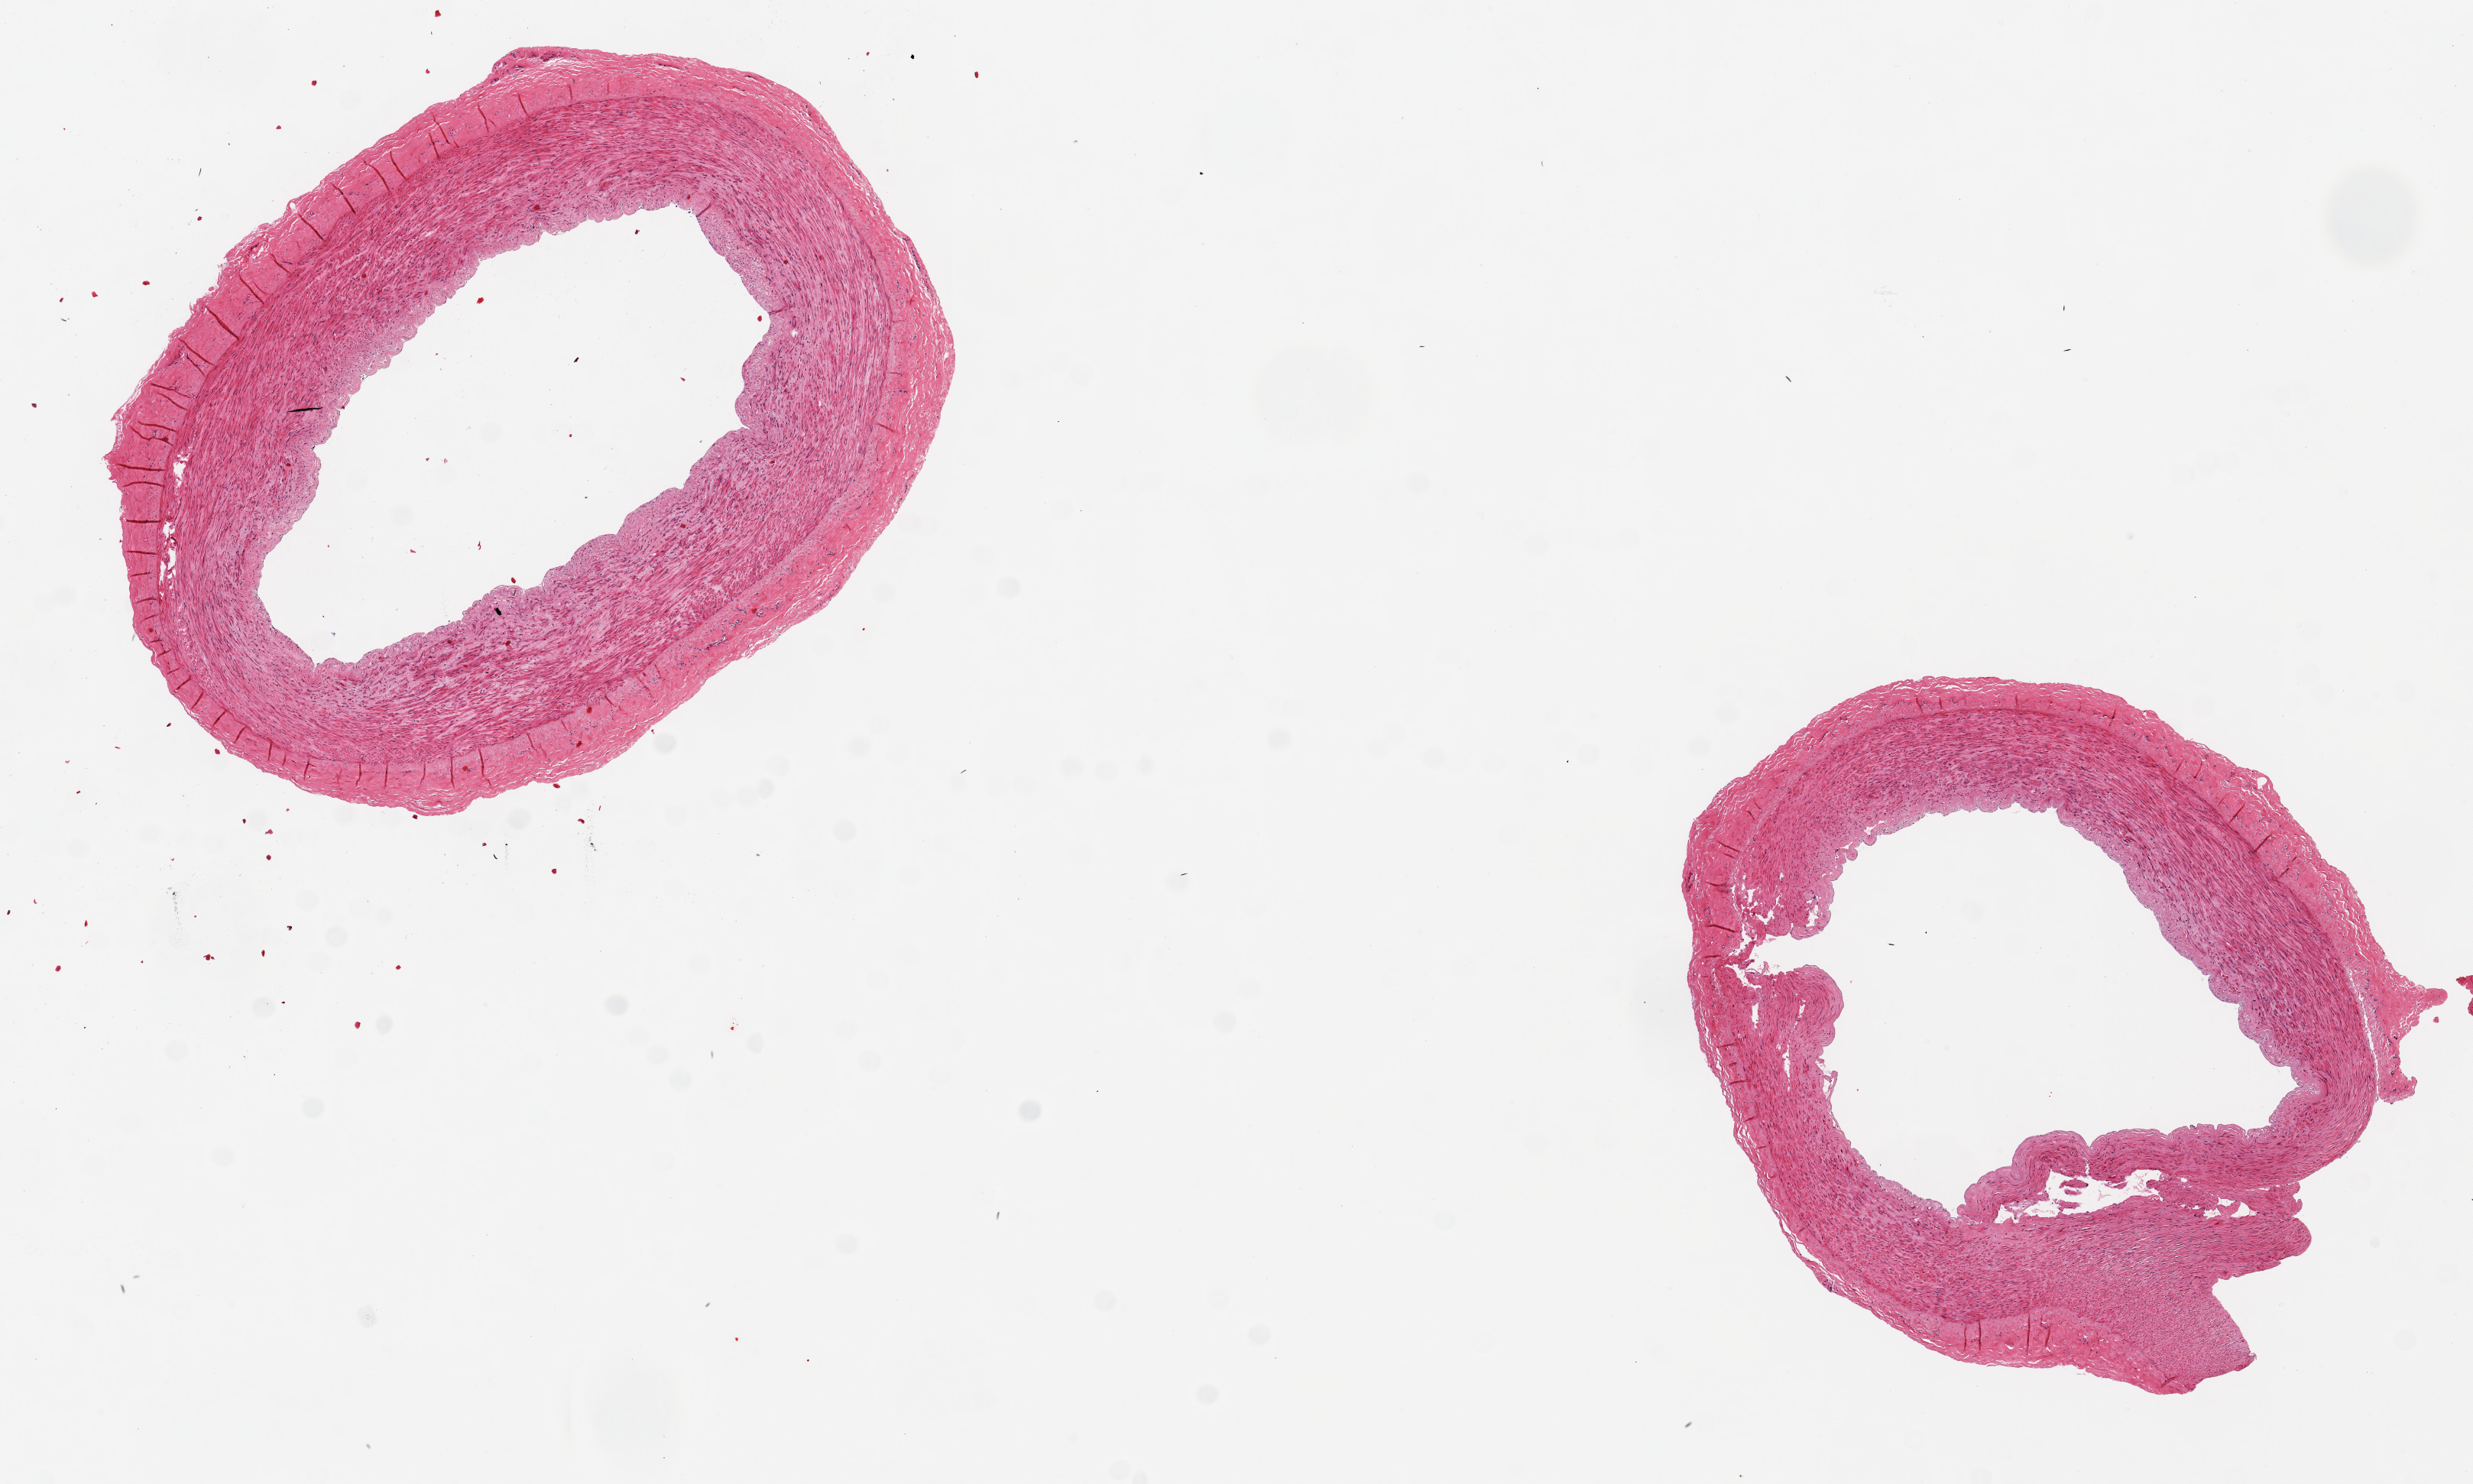
Whole-slide image, H&E stain, brightfield, a low-resolution overview of the entire scanned area, about 12.8 x 7.7 mm. PAXgene-fixed, paraffin-embedded tissue. Sampled site (target tissue): tibial artery. Donor tissue sample. Donor sex: male.
Pathologist's review note for this sample: 2 pieces, 4x3 & 4x4mm; No plaques, no extraneous tissue.